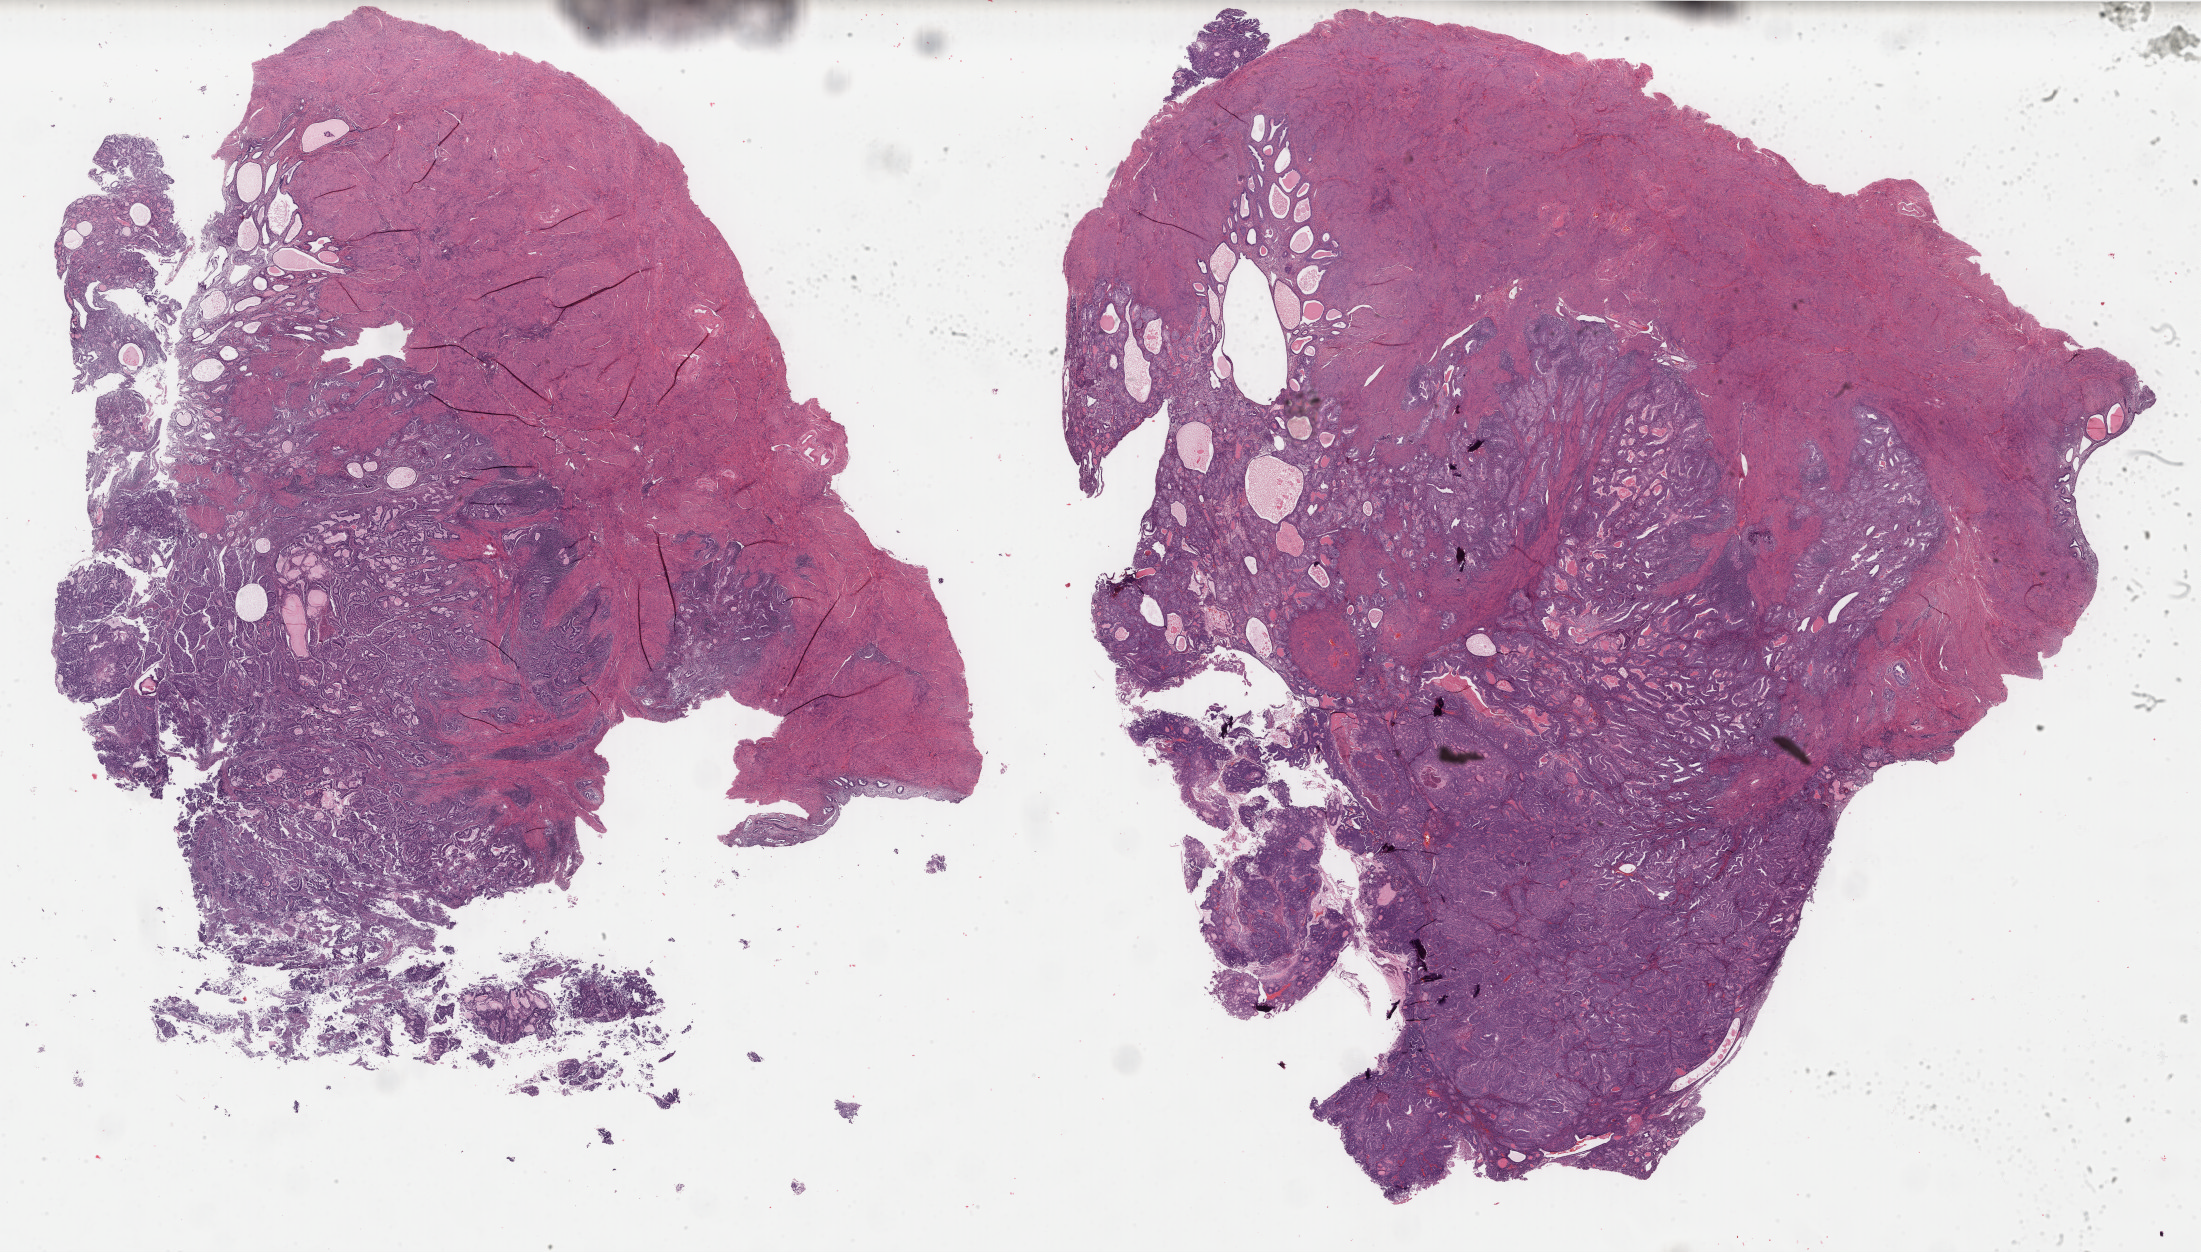
Digitized H&E-stained tissue section (whole slide) — low-resolution overview of the scanned area, about 34.9 x 19.9 mm (slide scanned at 40x), formalin-fixed paraffin-embedded (FFPE) diagnostic section, uterus, primary tumour sample. Patient: female, age at initial diagnosis 70 years. Histologic grade: G2 (moderately differentiated).
• diagnosis: Endometrioid adenocarcinoma, NOS (endometrium)
• FIGO stage: IB